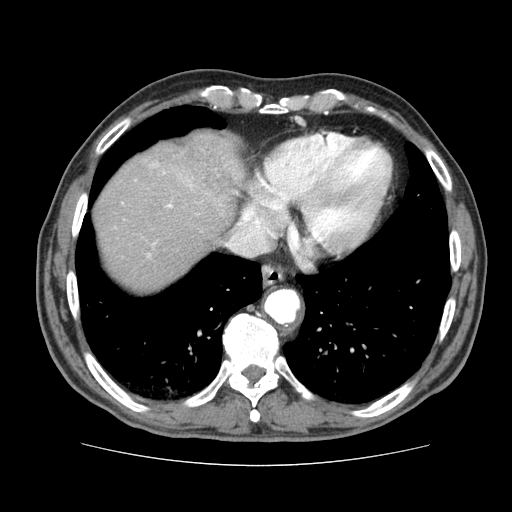
Contrast-enhanced abdominal CT (liver protocol), one axial slice. Position 70 of 79 along the scan axis. Reconstruction kernel STANDARD. 120 kVp. Soft-tissue window (W 400 / L 40 HU). 512 × 512 image matrix, field of view 360 × 360 mm. From the clinical record (not read from this slice): diagnosis: hepatocellular carcinoma (patient treated with transarterial chemoembolisation; whether this scan precedes or follows treatment is not stated here); TNM stage (as recorded): Stage-I; Child-Pugh class: A.
Annotated regions visible in this slice (semi-automatically segmented with operator editing):
- abdominal aorta: bounding box <267,290,300,323> (left, top, right, bottom; pixels)
- liver parenchyma outside the tumour (the mass and vessels are separate outlines, so this box may not span the whole liver): <94,136,244,290>
- mass: <143,131,242,217>
- liver vessels: <148,204,173,257>